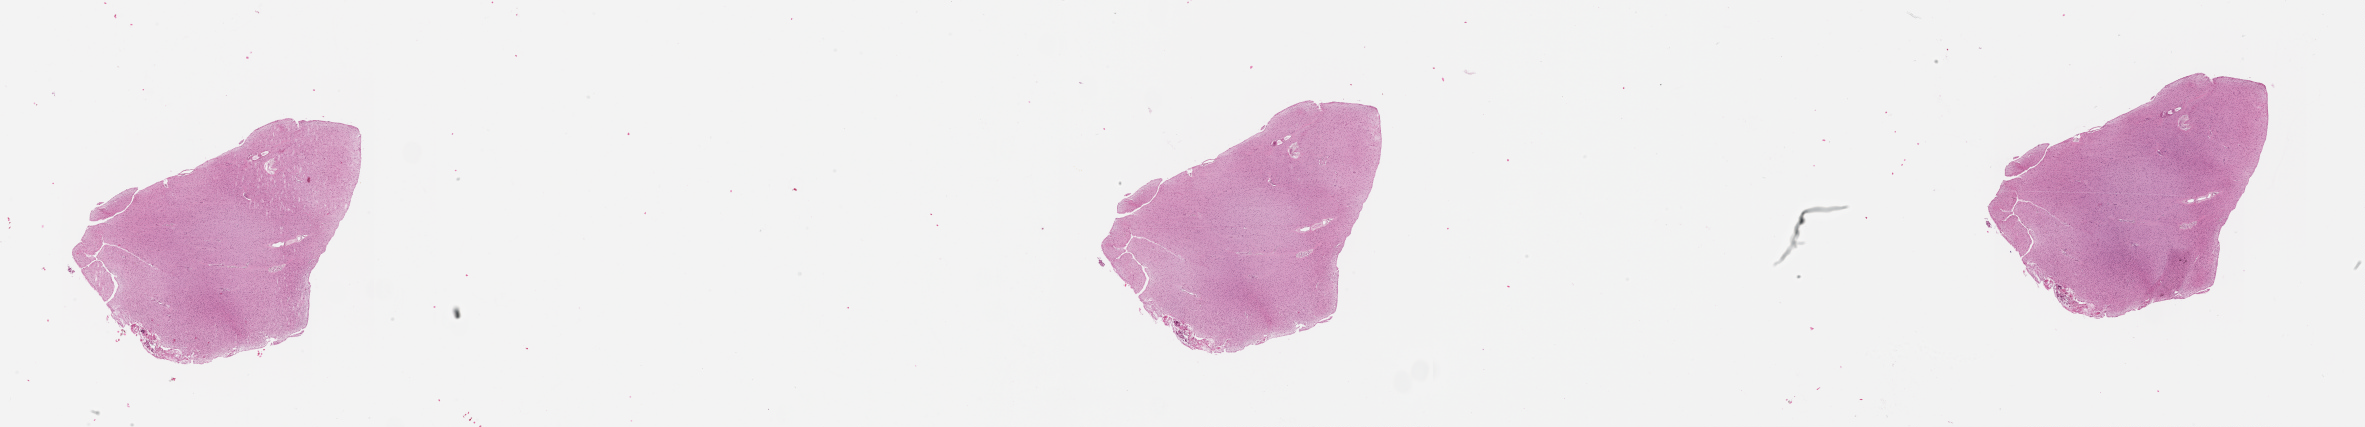
Hematoxylin and eosin (H&E) stained whole-slide image — low-resolution overview of the scanned area, about 38.1 x 6.9 mm (slide scanned at 20x), tumour tissue sample, sampled site: frontal lobe. 60-year-old male patient. Slide review estimates, as recorded: tumour nuclei 60%, necrosis 5%.
• primary tumour site (as recorded): frontal lobe
• histologic diagnosis: Glioblastoma